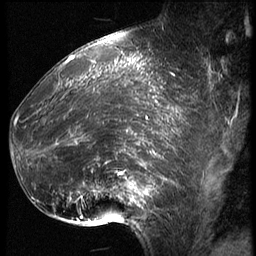
Breast MRI (dynamic contrast-enhanced), one sagittal slice. Slice 23 of 62 in the series (ordered by position). 3 images stored at this slice position (order not interpretable as contrast timing). 1.5 T. TE 4.2 ms, TR 9 ms. 256 × 256 image matrix. Patient: female, 39 years. Case-level facts recorded for this patient, not image findings: setting: breast cancer imaged before/during neoadjuvant chemotherapy; receptor status: HER2-positive.
Outlined on this slice (semi-automatic segmentation, software-assisted and operator-edited):
- analysis volume of interest (the breast-tissue region the enhancement analysis was run in; not a lesion): bounding box (x1, y1, x2, y2) in pixels: (16, 64, 171, 228)
- tumour enhancement mask (voxels above the 140 % enhancement threshold inside the analysis volume of interest): (16, 64, 171, 224)